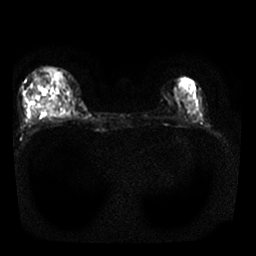
Breast MRI, one axial slice. Slice 10 of 25 in the series (ordered by position). Diffusion-weighted series; image 2 of 4 stored at this slice position (different b-values; order by instance number). 1.5 T. 4 mm slice thickness. 256 × 256 image matrix. Female patient.
Annotated regions visible in this slice (manually delineated by an expert):
- tumour on diffusion-weighted imaging: box from (x=45, y=102) to (x=56, y=114) px